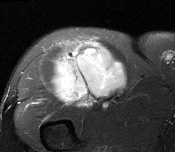
MRI of an extremity soft-tissue mass, one axial slice. T2-weighted fat-saturated. MR volume resampled by the dataset authors to the PET/CT grid (not the native acquisition matrix). 3.27 mm slice thickness. 175 × 152 image matrix, field of view 171 × 148 mm. Male patient. From the clinical record (not read from this slice): histological type: pleiomorphic leiomyosarcoma; grade: intermediate; site of the primary tumour: right thigh.
Outlined on this slice (expert contour drawn on MRI and transferred to this co-registered scan by the dataset authors):
- gross tumour volume including surrounding oedema: bounding box [x1, y1, x2, y2] px = [54, 40, 126, 103]
- gross tumour volume (mass): [56, 42, 126, 103]